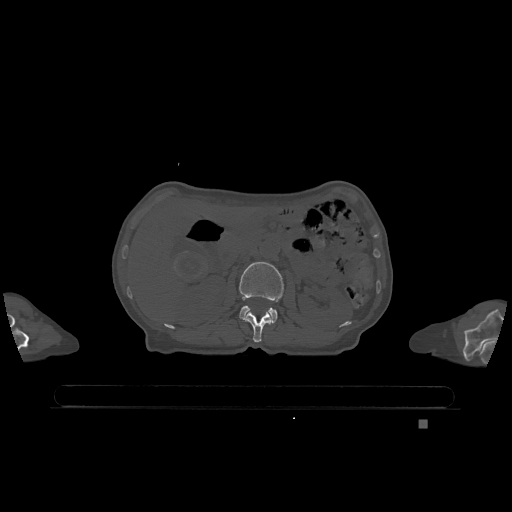
CT including the spine, one axial slice; position 442 of 1317 along the scan axis; bone window (W 1800 / L 400 HU); 512 × 512 image matrix, field of view 500 × 500 mm. Female patient, age 74 years. From the clinical record (not read from this slice): primary cancer: lung.
Outlined on this slice (semi-automatic segmentation, software-assisted and operator-edited):
- L1 vertebra: bounding box <244,312,272,343> (left, top, right, bottom; pixels)
- L2 vertebra: <239,262,284,323>